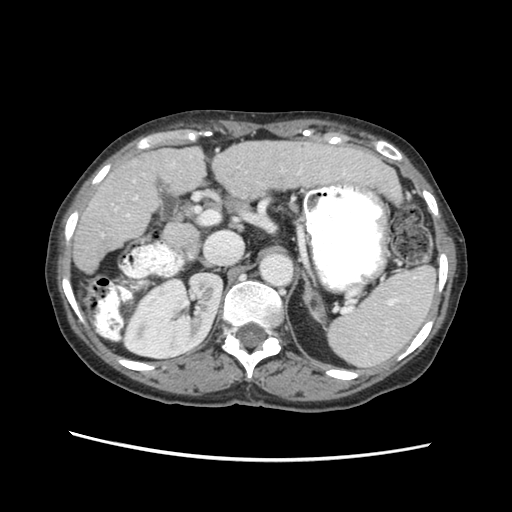
Contrast-enhanced abdominal CT (liver protocol), one axial slice; position 31 of 63 along the scan axis; soft-tissue window (W 400 / L 40 HU); 2.5 mm slice thickness; 512 × 512 image matrix. Case-level facts recorded for this patient, not image findings: diagnosis: hepatocellular carcinoma (patient treated with transarterial chemoembolisation; whether this scan precedes or follows treatment is not stated here); TNM stage (as recorded): Stage-I; Child-Pugh class: B; tumour differentiation: well differentiated.
Structures marked on this image (semi-automatic segmentation, software-assisted and operator-edited):
- liver parenchyma outside the tumour (the mass and vessels are separate outlines, so this box may not span the whole liver): bounding box <74,138,400,272> (left, top, right, bottom; pixels)
- liver vessels: <102,161,343,235>